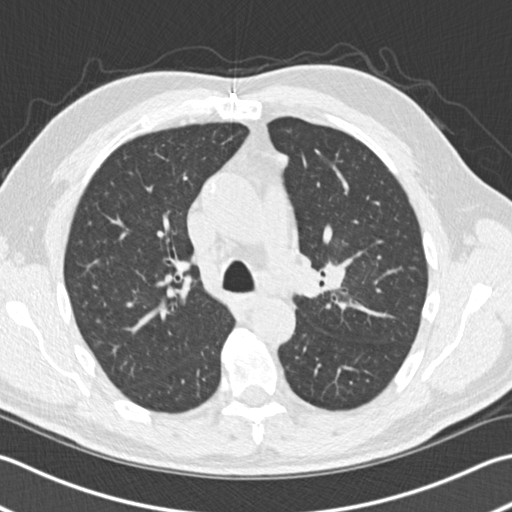
Low-dose screening chest CT, one axial slice; position 102 of 153 along the scan axis; reconstruction kernel B30f; 120 kVp; lung window (W 1500 / L -600 HU); 512 × 512 image matrix, field of view 346 × 346 mm.
Outlined on this slice (expert manual segmentation):
- lesion 1 (tumor, upper lobe of left lung): box from (x=326, y=265) to (x=346, y=289) px